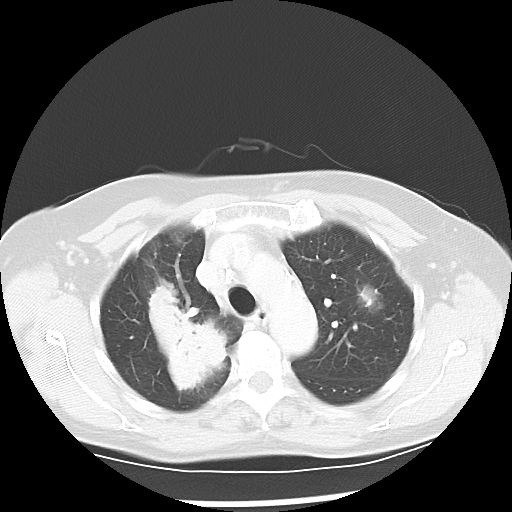
Chest CT, one axial slice; position 38 of 52 along the scan axis; reconstruction kernel LUNG; lung window (W 1500 / L -600 HU); 5 mm slice thickness; 512 × 512 image matrix, field of view 328 × 328 mm. Patient: female, 60 years. From the clinical record (not read from this slice): clinical TNM (as recorded): T2 N1 M1a.
Outlined on this slice (bounding box drawn by a radiologist):
- lung tumour (recorded histology: adenocarcinoma): box from (x=134, y=279) to (x=228, y=406) px